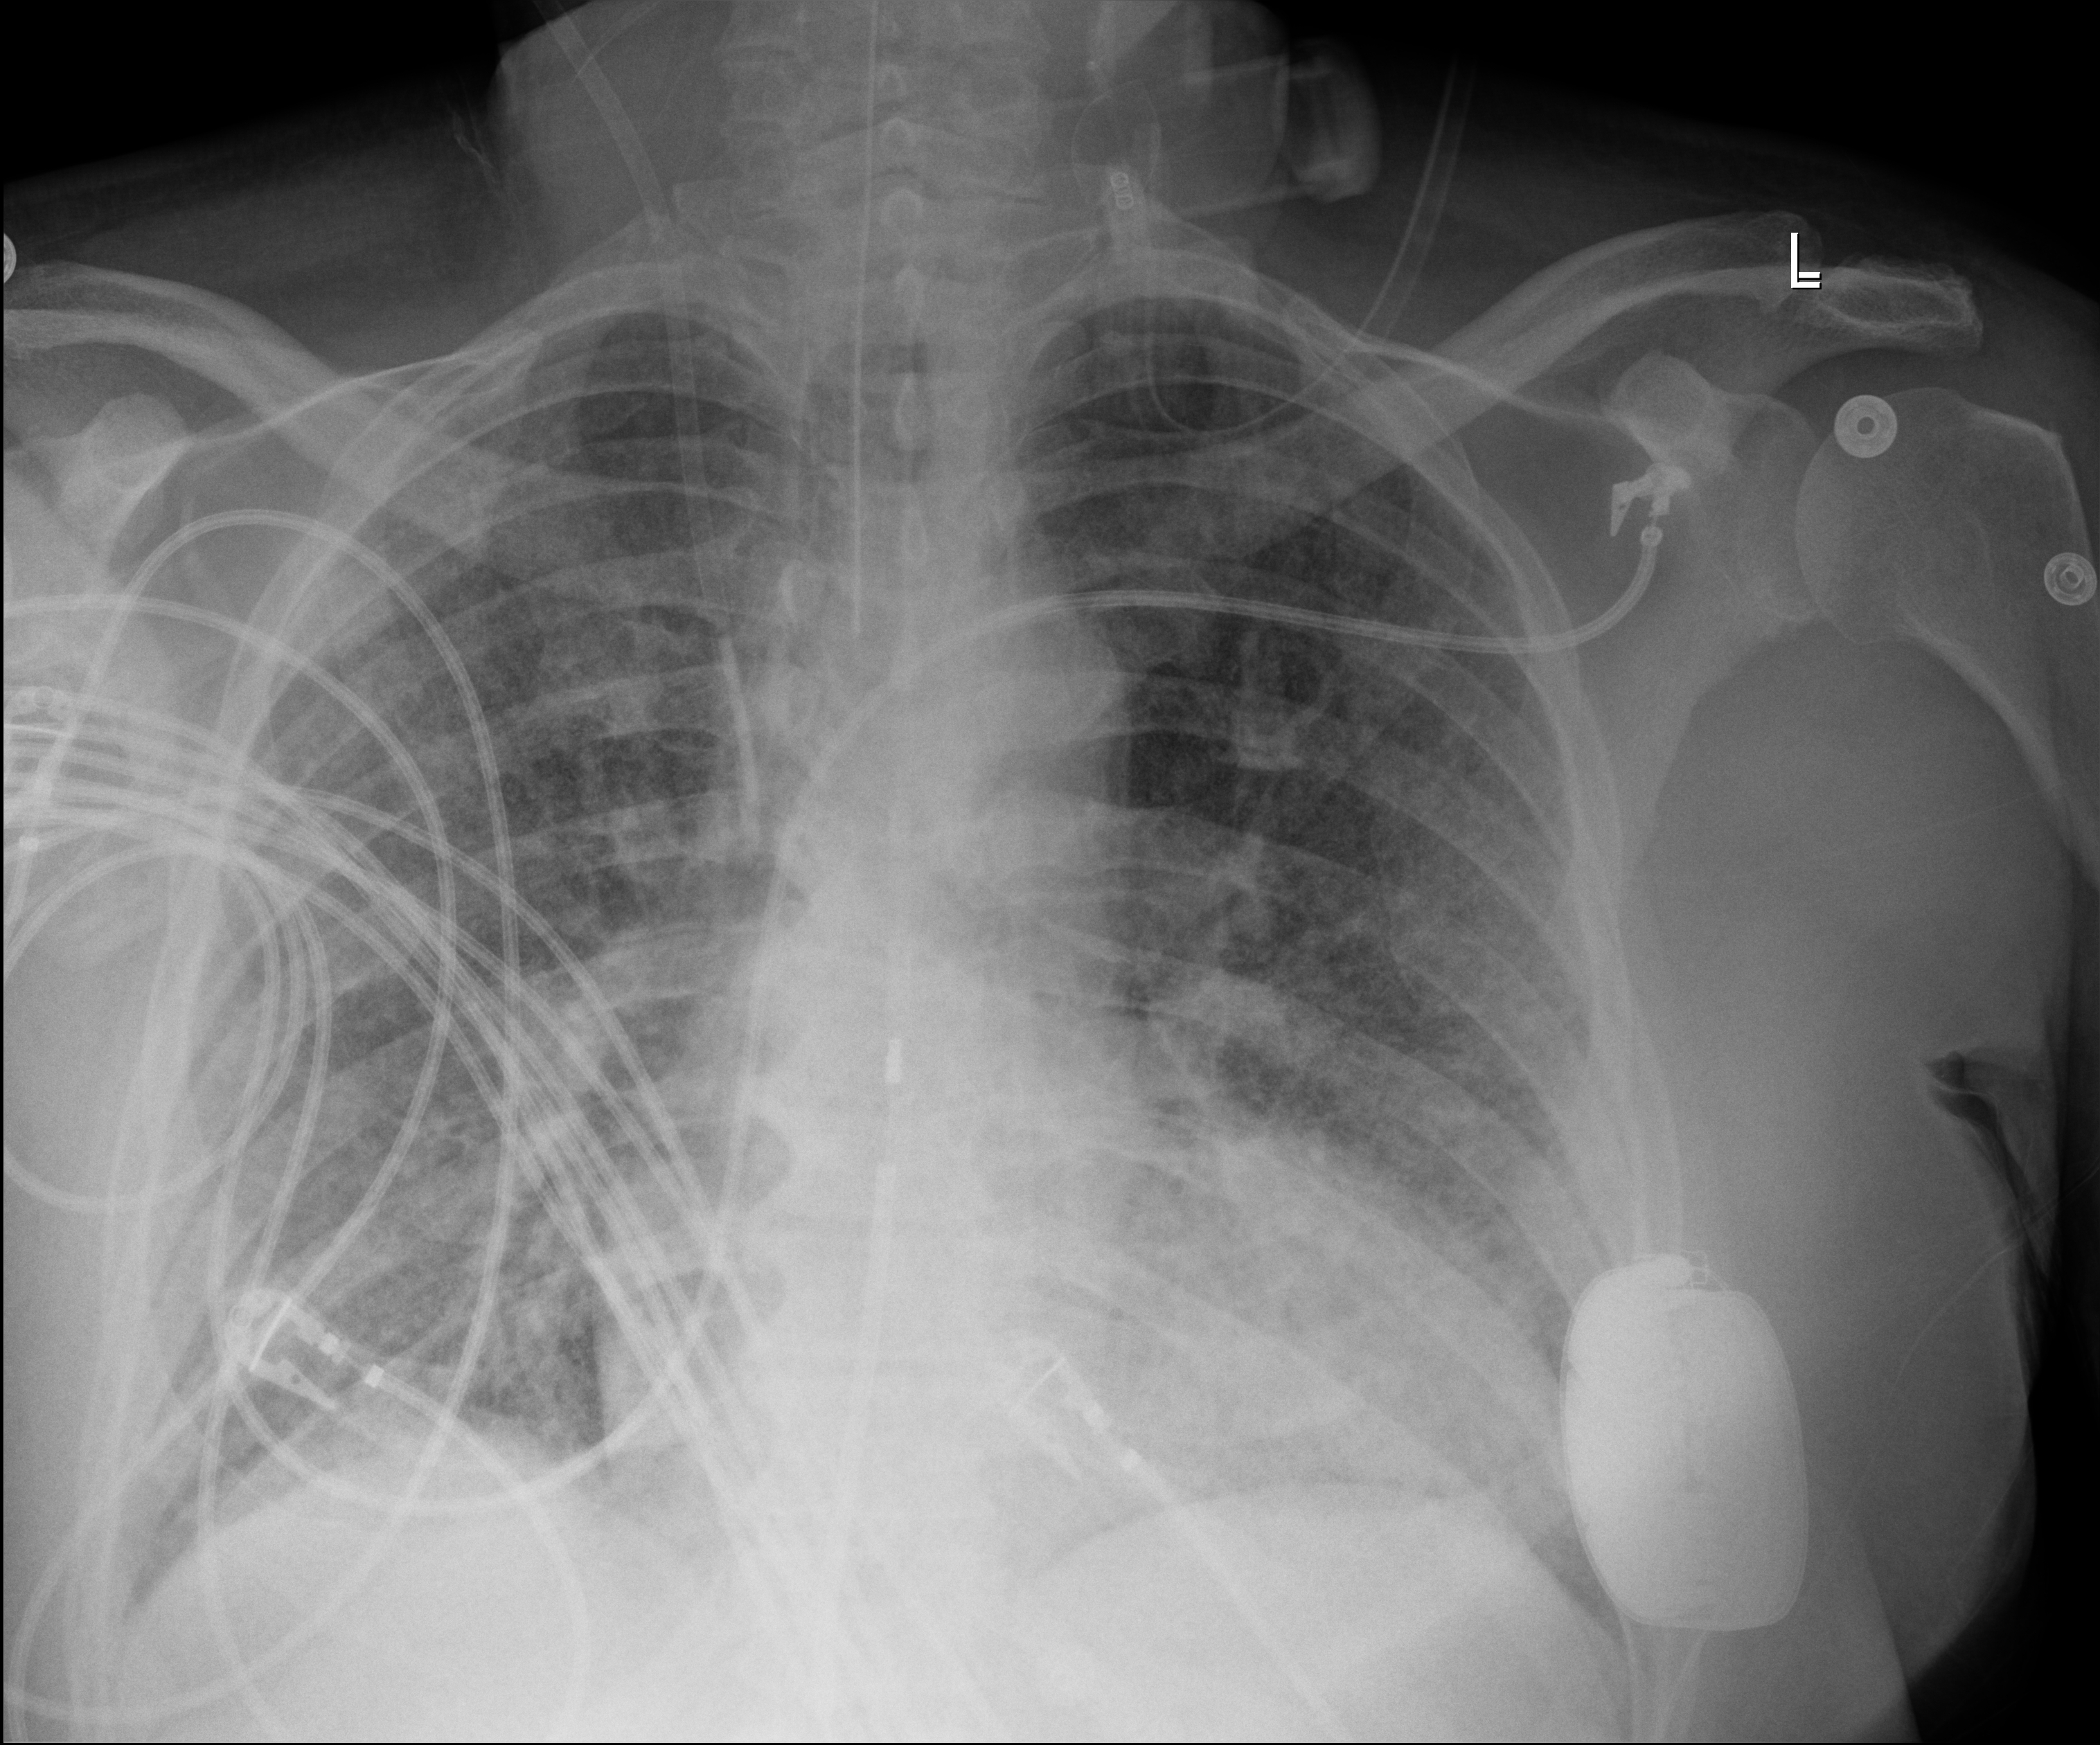
Bedside chest radiograph (digital radiography), anteroposterior (AP) projection. Patient hospitalised with COVID-19; male, aged 60–74 years.
Admission-level facts for this patient (not findings on this image; timing relative to this image not recorded):
- smoking status (admission record): never
- chronic kidney disease (admission record): no